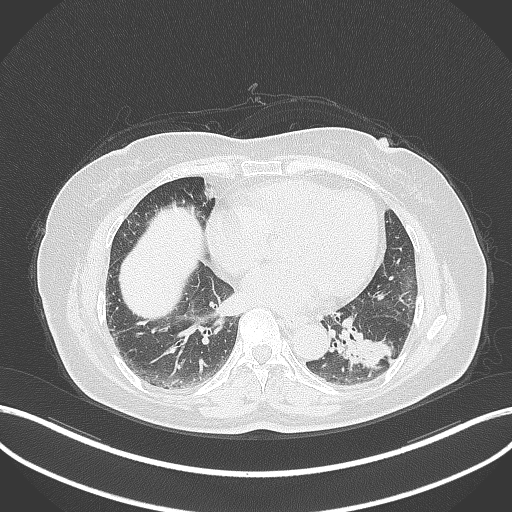
Chest CT, one axial slice. Slice 148 of 311 in the series (ordered by position). 120 kVp. Lung window (W 1500 / L -600 HU). 1 mm slice thickness. 512 × 512 image matrix, field of view 400 × 400 mm. Patient: female, 59 years. From the clinical record (not read from this slice): clinical TNM (as recorded): T2a N0 M0; histopathological grade: G2-3.
Structures marked on this image (rectangle marked by the reading radiologist):
- lung tumour (recorded histology: adenocarcinoma): bounding box (x1, y1, x2, y2) in pixels: (345, 321, 393, 371)